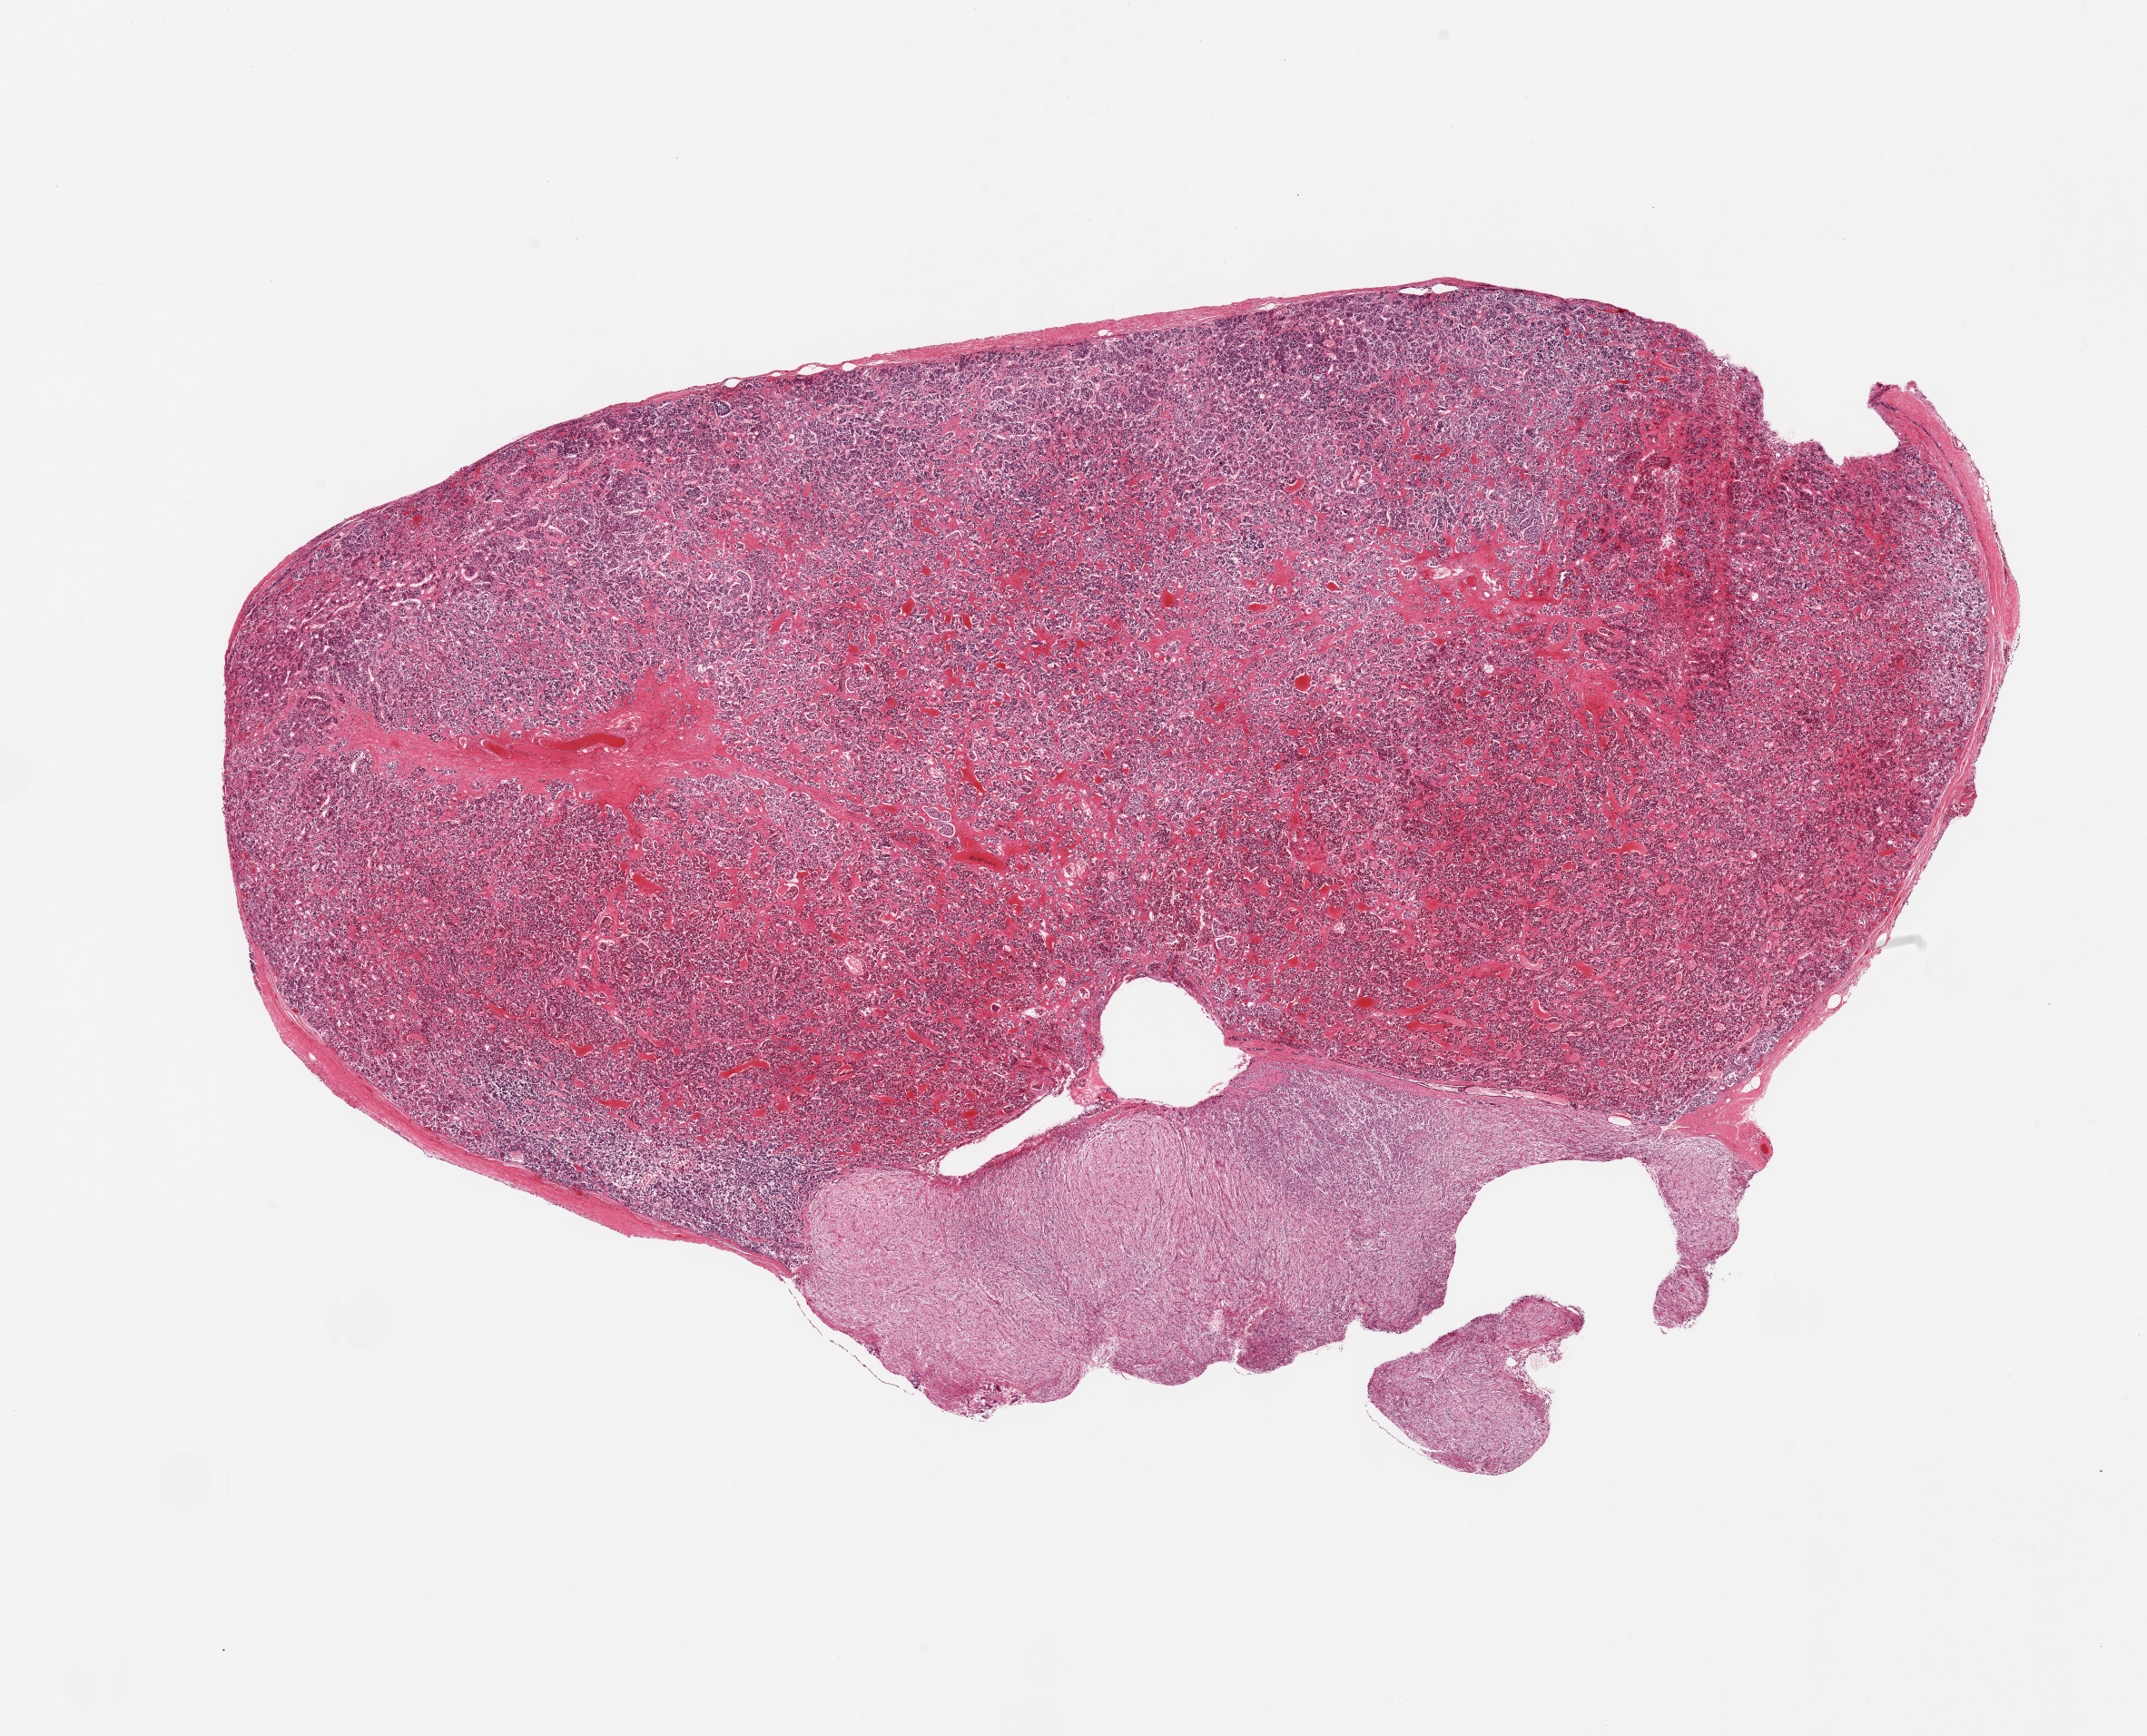
Digitized H&E-stained section, brightfield — a low-resolution overview of the entire scanned area, about 18.7 x 15.1 mm (slide scanned at 20x). PAXgene-fixed paraffin-embedded (PFPE) section. Target tissue: pituitary. Tissue donor sample. Male donor.
Review note (as recorded): 1 piece; 15% neurohypophysis.